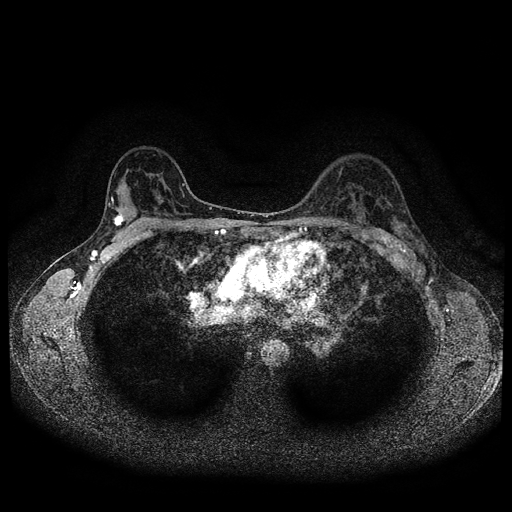
Breast MRI (dynamic contrast-enhanced, multi-phase), one axial slice. Position 67 of 116 along the scan axis. Dynamic contrast-enhanced series, time point 2 of 5 at this slice position (early post-contrast). 1.5 T. TE 2.7 ms, TR 5.4 ms. 2 mm slice thickness. 512 × 512 image matrix, field of view 330 × 330 mm. Female patient, age 36 years.
Structures marked on this image (semi-automatically segmented with operator editing):
- breast lesion (labelled 'tumour' in the annotation; benign lesions carry a separate 'benign' label): bounding box [x1, y1, x2, y2] px = [111, 212, 125, 229]